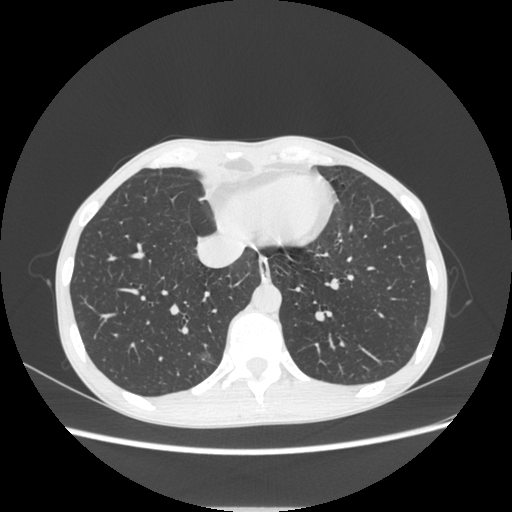
Chest CT, one axial slice; position 83 of 272 along the scan axis; lung window (W 1500 / L -600 HU); 1.25 mm slice thickness; 512 × 512 image matrix, field of view 350 × 350 mm. Patient: female, 51 years. From the clinical record (not read from this slice): clinical TNM (as recorded): T1c N0 M0.
Outlined on this slice (rectangle marked by the reading radiologist):
- lung tumour (recorded histology: adenocarcinoma): bounding box <191,344,220,374> (left, top, right, bottom; pixels)